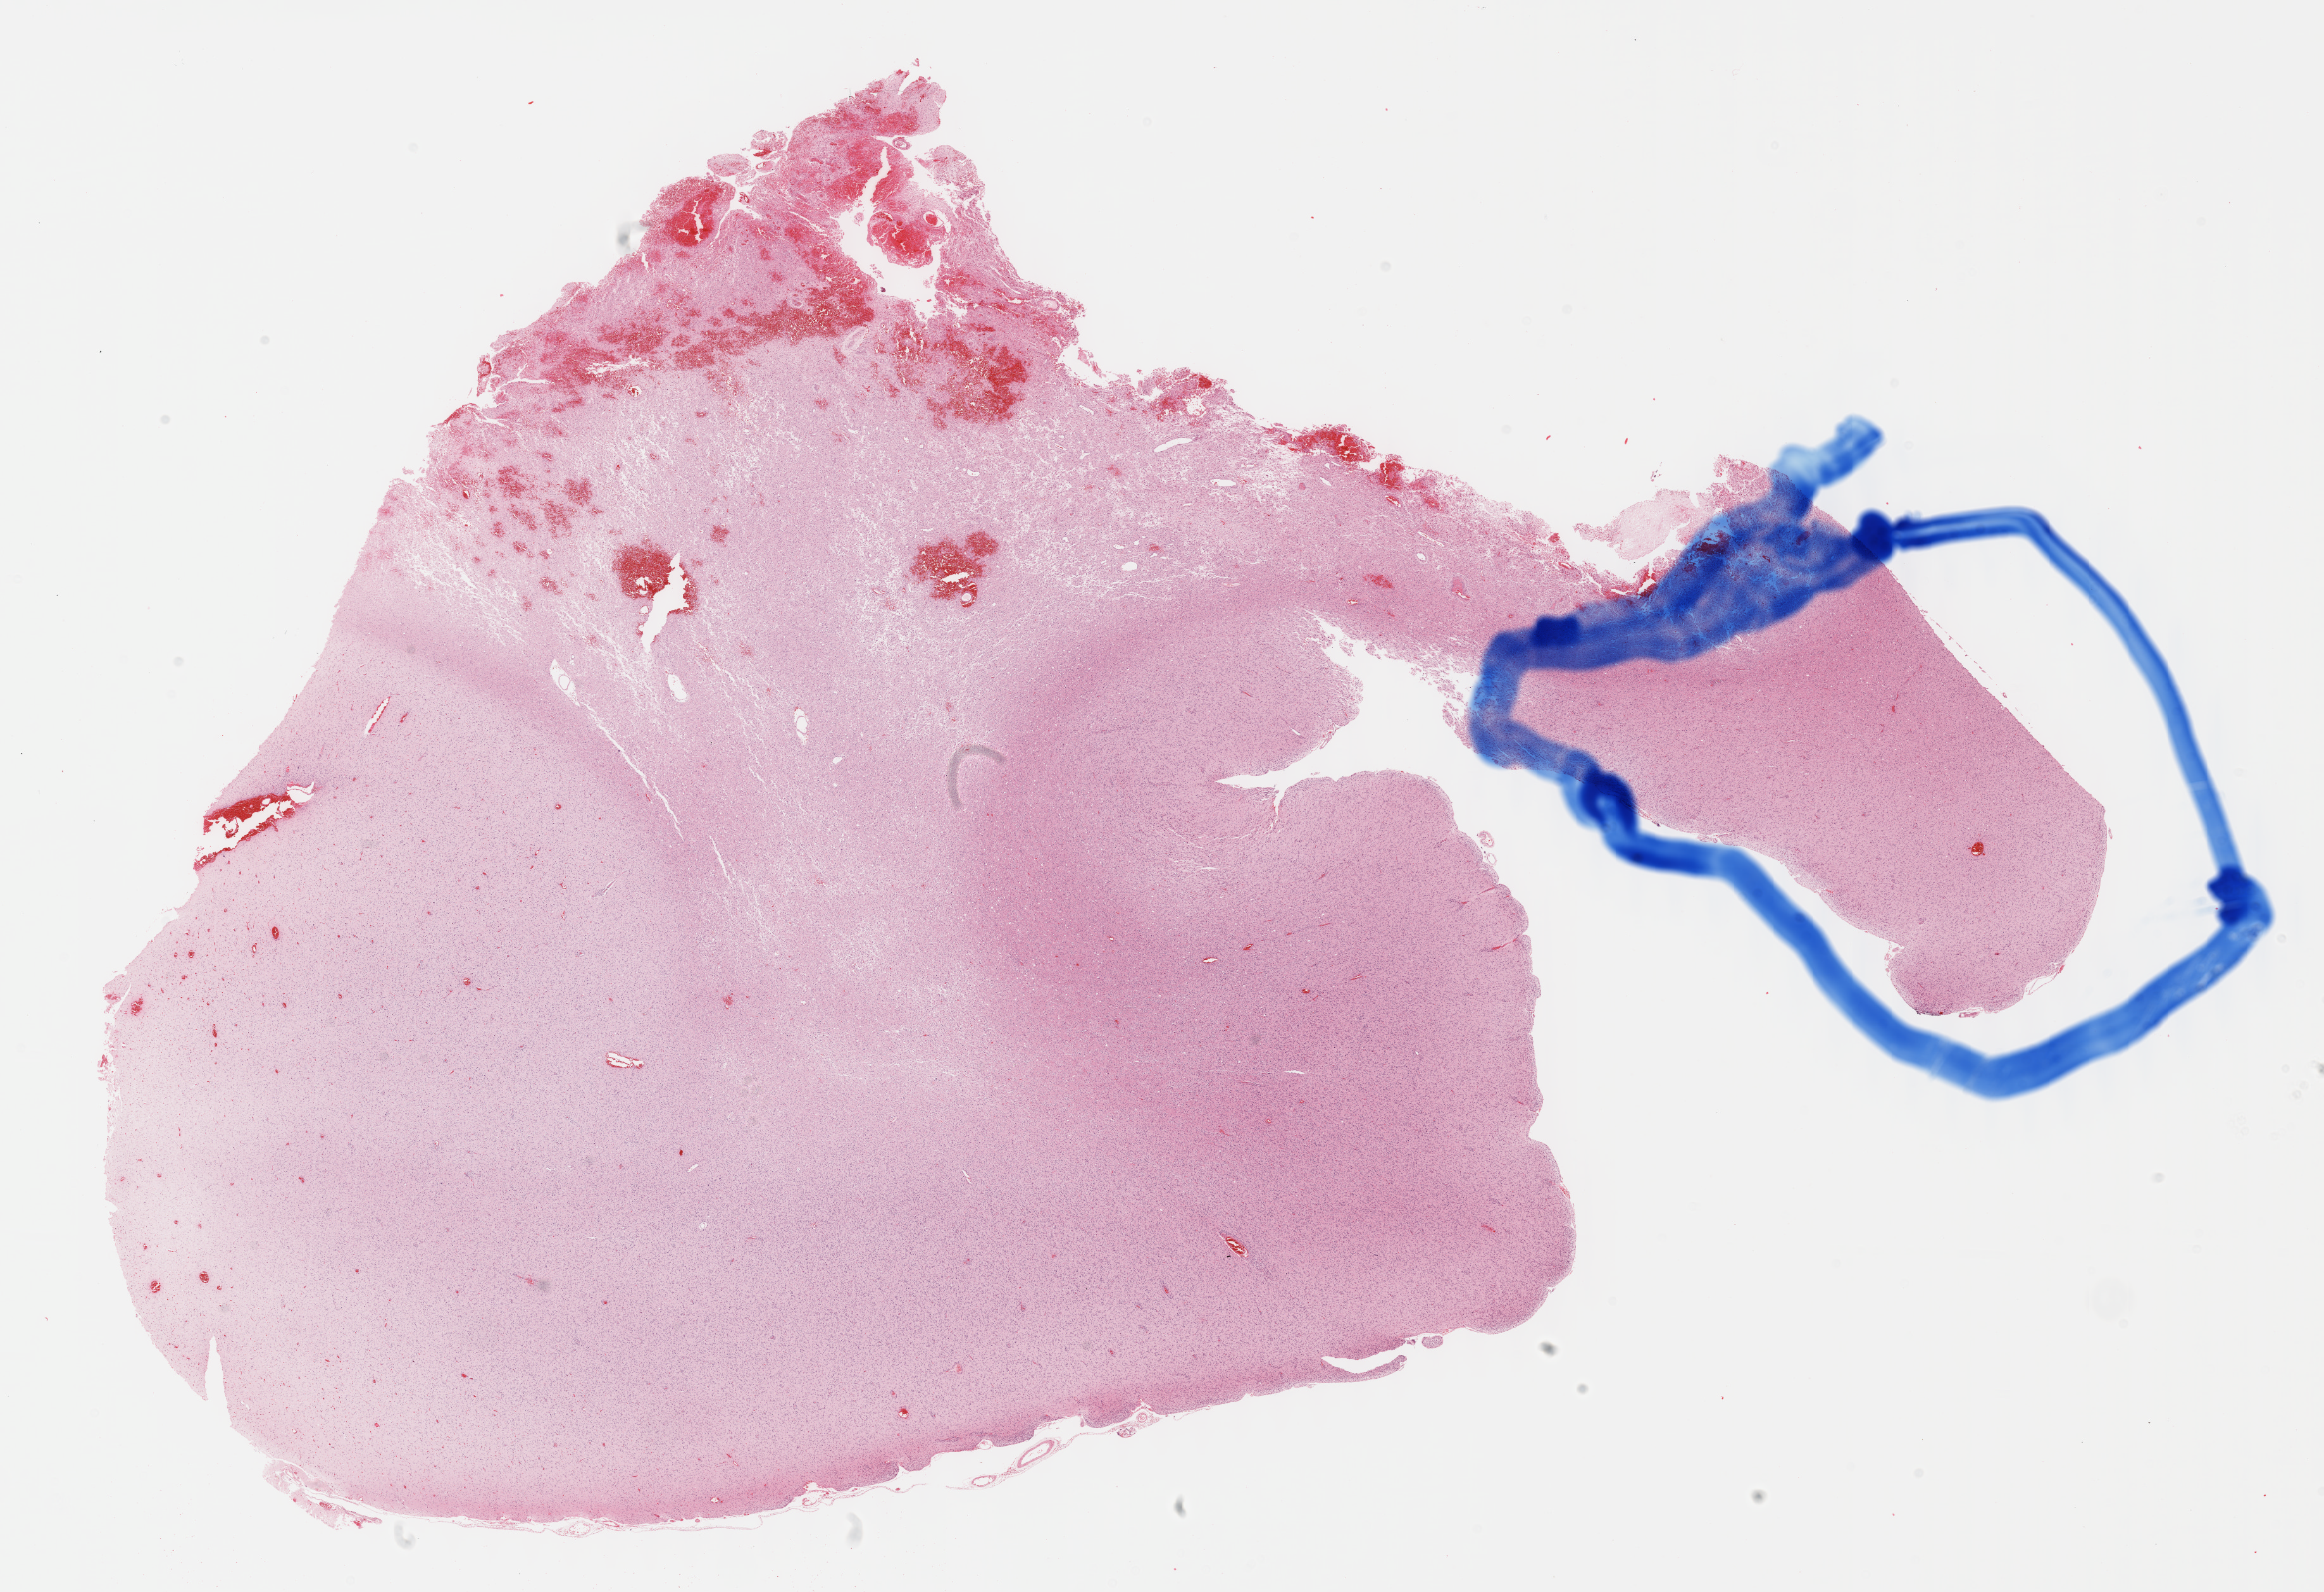
Digitized Hematoxylin and eosin (H&E) stained tissue section (whole slide), low-resolution overview of the scanned area, about 29.7 x 20.3 mm (slide scanned at 40x), formalin-fixed paraffin-embedded (FFPE) diagnostic section, brain, primary tumour sample. Female, age 74 years at initial diagnosis.
Diagnosis: Glioblastoma.